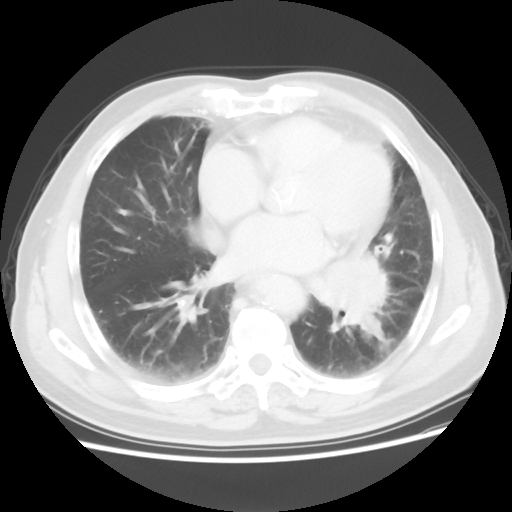
Chest CT, one axial slice. Slice 26 of 56 in the series (ordered by position). Lung window (W 1500 / L -600 HU). 5 mm slice thickness. 512 × 512 image matrix. Male patient, age 75 years. Case-level facts recorded for this patient, not image findings: clinical TNM (as recorded): T3 N0 M0.
Annotated regions visible in this slice (bounding box drawn by a radiologist):
- lung tumour (recorded histology: squamous cell carcinoma): bounding box <313,250,397,338> (left, top, right, bottom; pixels)